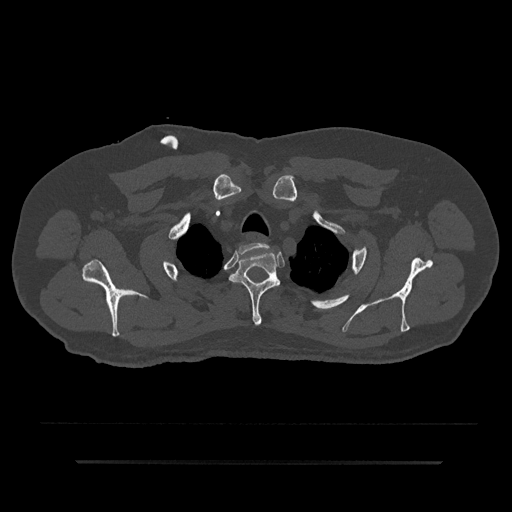
CT including the spine, one axial slice. Slice 698 of 797 in the series (ordered by position). Reconstruction kernel Br40s/3. 120 kVp. Bone window (W 1800 / L 400 HU). 0.5 mm slice thickness. 512 × 512 image matrix, field of view 464 × 464 mm. Male patient, age 59 years. From the clinical record (not read from this slice): primary cancer: bile ducts; vertebrae with lytic lesions (as recorded): T10.
Outlined on this slice (semi-automatic segmentation, software-assisted and operator-edited):
- T1 vertebra: bounding box <239,243,269,256> (left, top, right, bottom; pixels)
- T2 vertebra: <229,252,280,326>